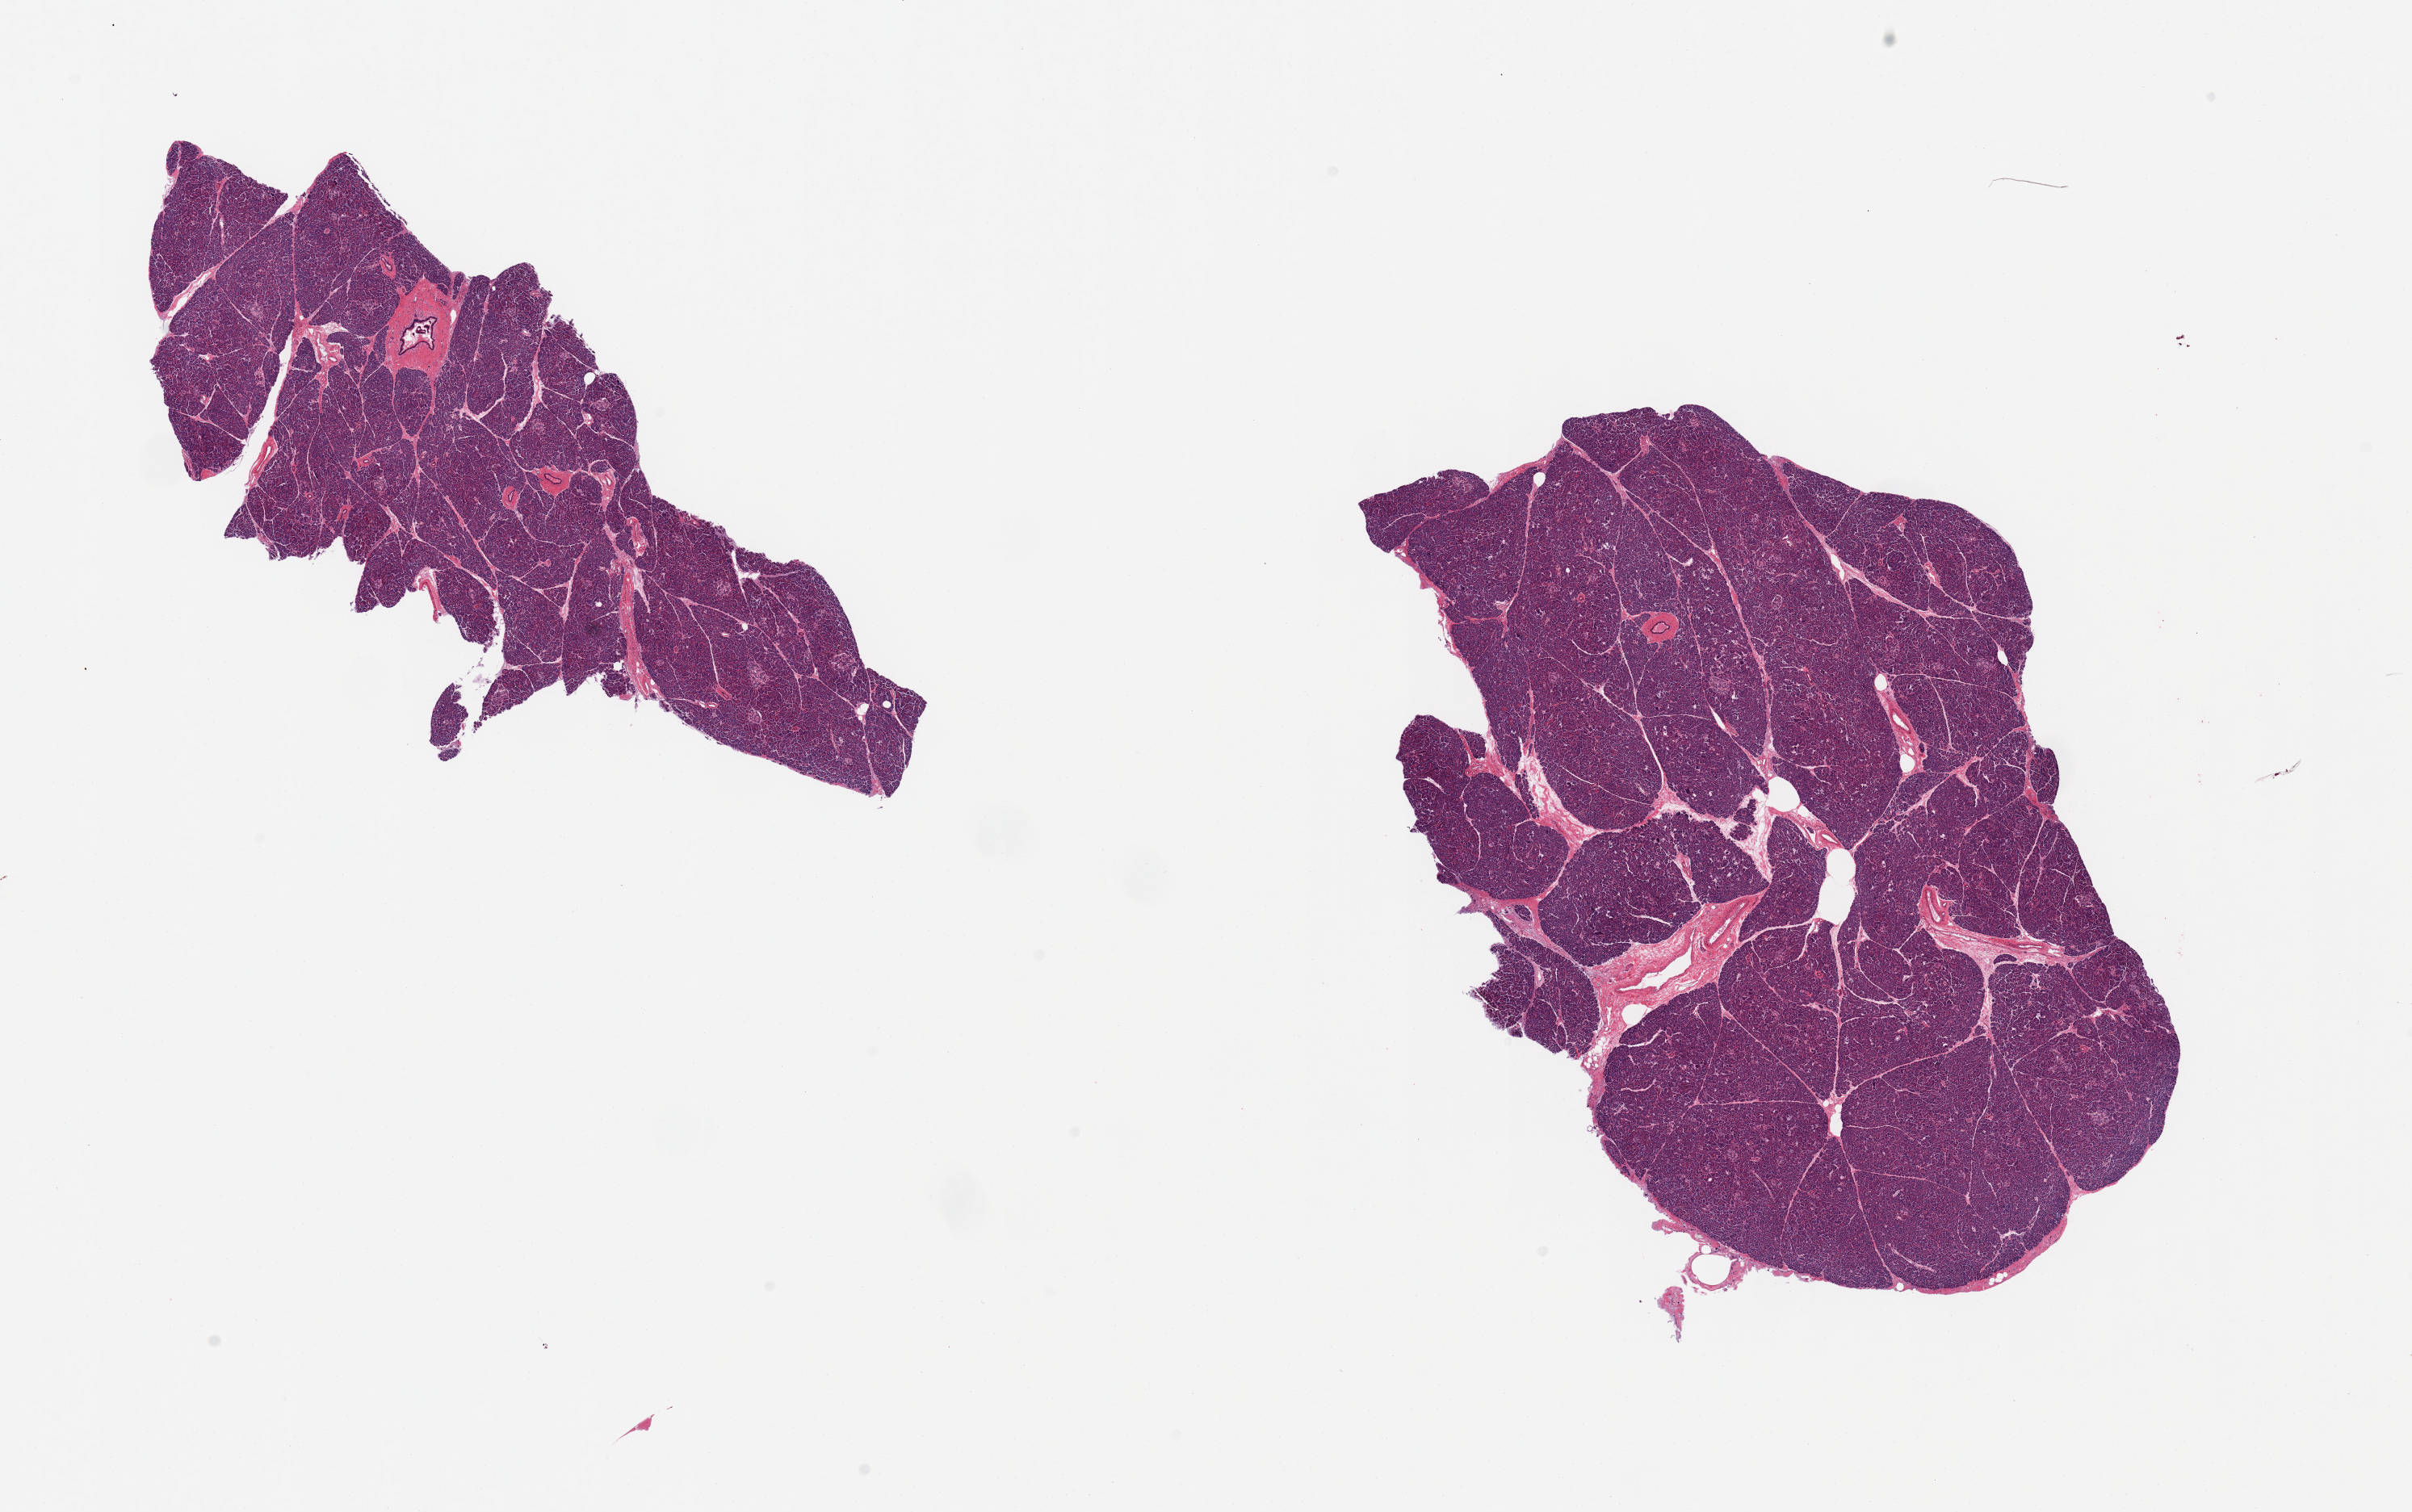
Digitized haematoxylin and eosin-stained section — a low-resolution overview of the entire scanned area, about 23.6 x 14.8 mm. PAXgene-fixed paraffin-embedded (PFPE) section. Sampled site (target tissue): pancreas. Tissue donor sample. Male donor.
* reviewer comment on this tissue sample: 2 pieces, well- perserved, Islets well visualize